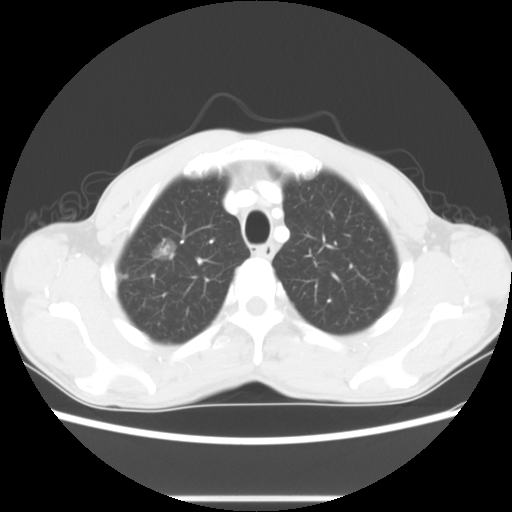
Chest CT, one axial slice. Position 59 of 73 along the scan axis. Reconstruction kernel STANDARD. Lung window (W 1500 / L -600 HU). 512 × 512 image matrix, field of view 350 × 350 mm. Male patient, age 54 years. Case-level facts recorded for this patient, not image findings: clinical TNM (as recorded): T1a N0 M0.
Structures marked on this image (bounding box drawn by a radiologist):
- lung tumour (recorded histology: adenocarcinoma): bounding box (x1, y1, x2, y2) in pixels: (142, 233, 180, 267)